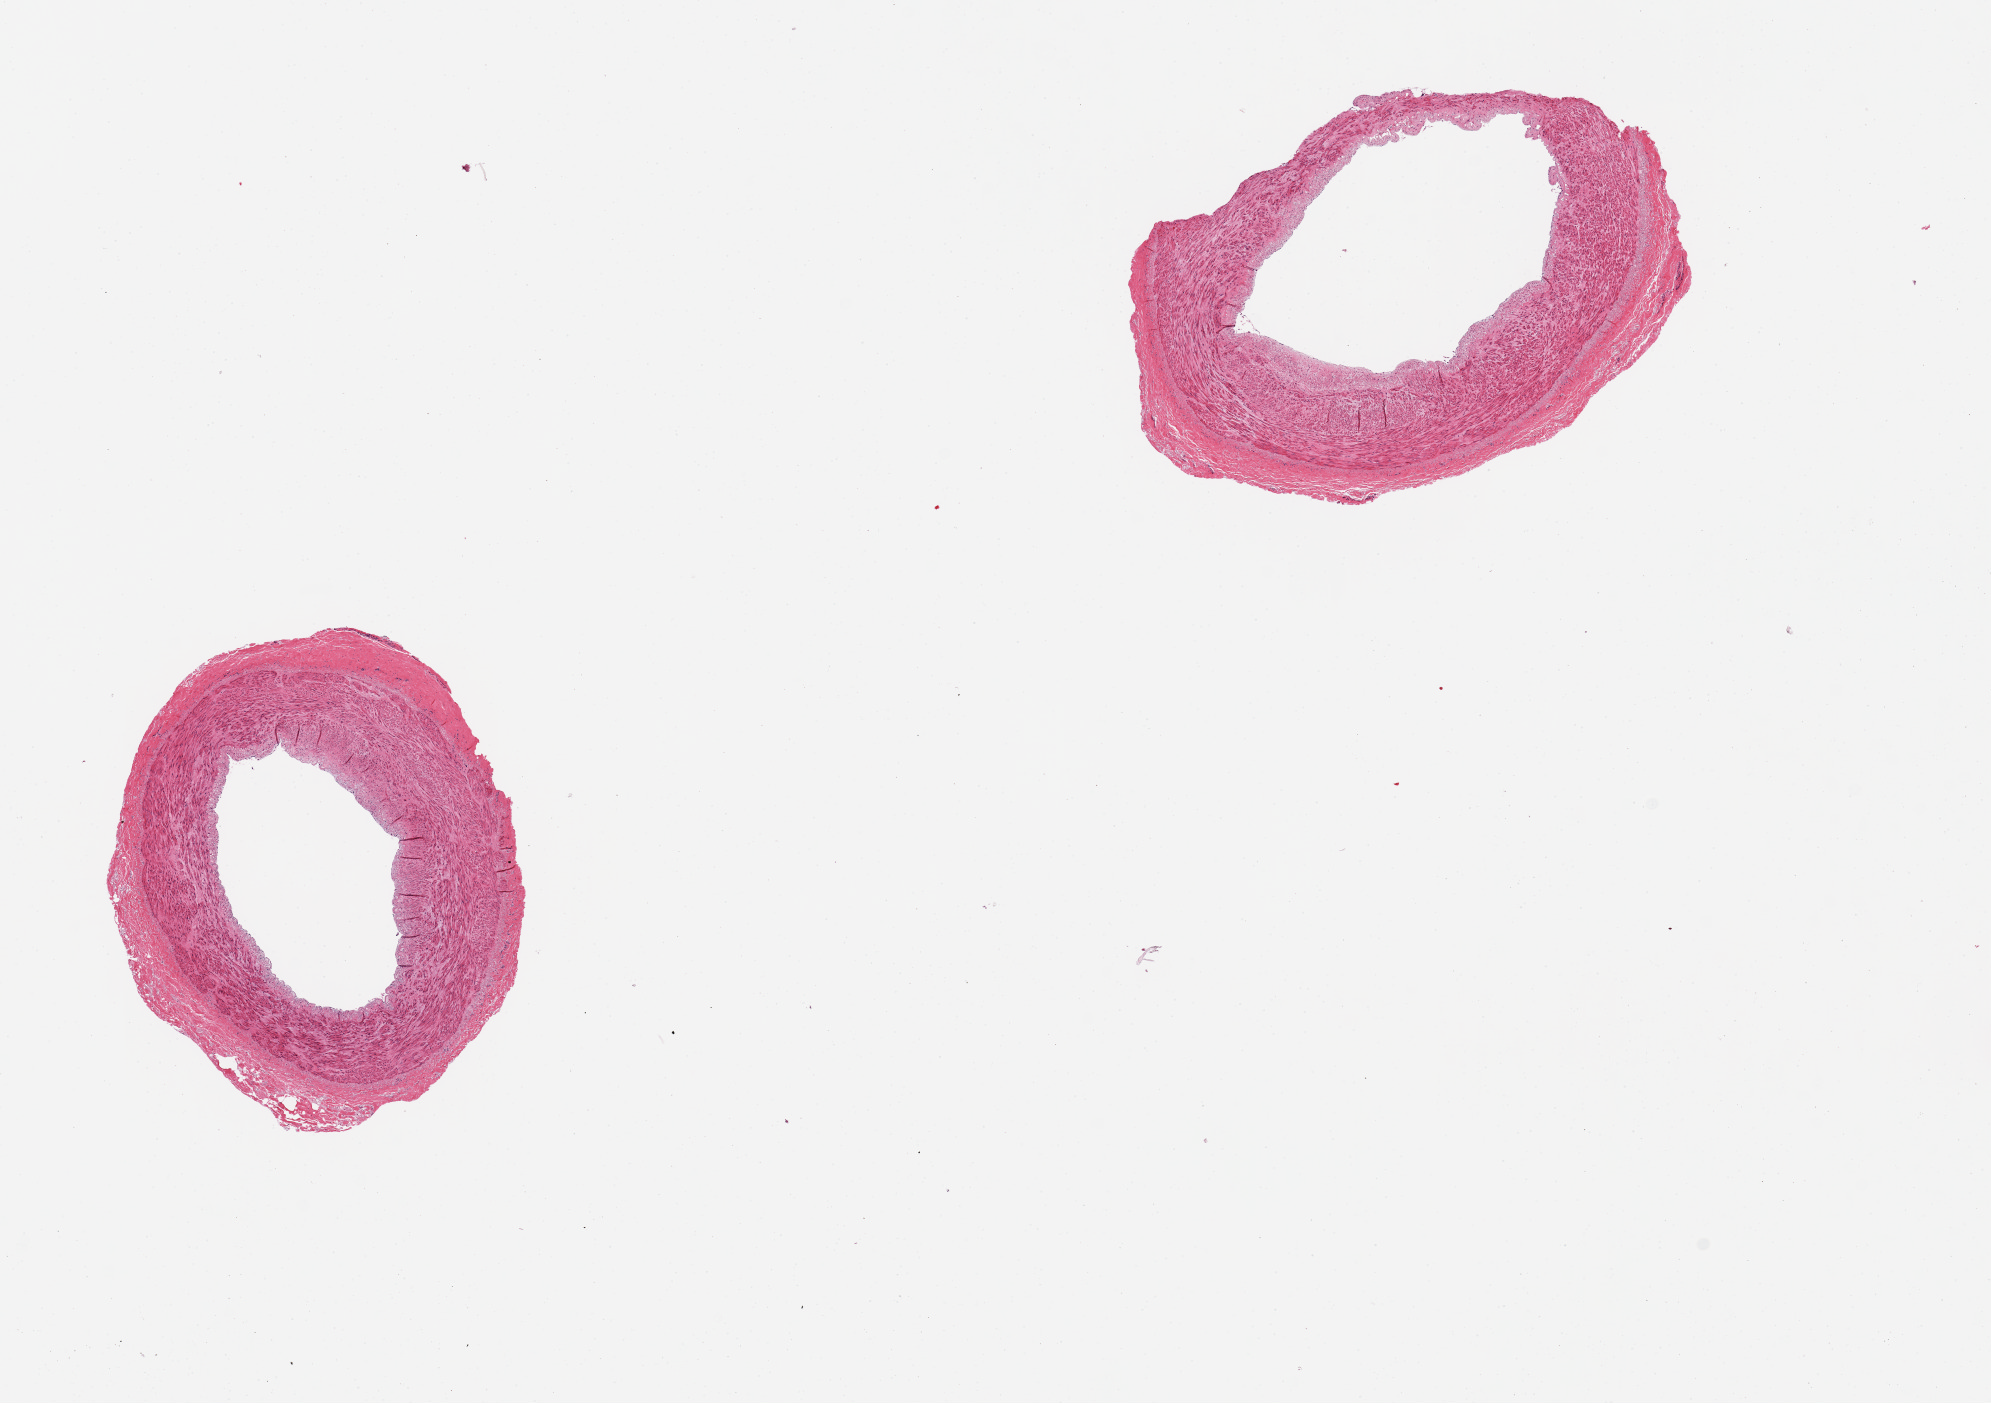
Digitized hematoxylin and eosin (H&E)-stained section, brightfield — low-resolution overview of the scanned area, about 15.8 x 11.1 mm, PAXgene-fixed paraffin-embedded (PFPE) section, sampled site (target tissue): tibial artery, tissue donor sample. Female donor.
• reviewer comment on this tissue sample: 2 pieces, clean specimens, no adherent fat